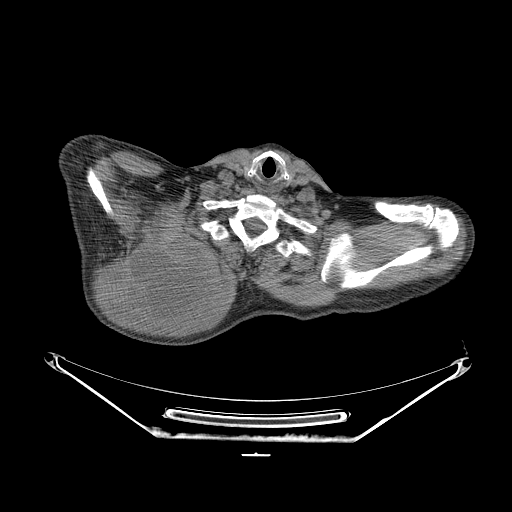
CT of an extremity soft-tissue mass (from a PET/CT study), one axial slice; slice 210 of 267 in the series (ordered by position); reconstruction kernel STANDARD; 140 kVp; soft-tissue window (W 400 / L 40 HU); 3.75 mm slice thickness; 512 × 512 image matrix, field of view 500 × 500 mm. Male patient. From the clinical record (not read from this slice): histological type: pleiomorphic spindle cell undifferentiated; grade: high; site of the primary tumour: right parascapusular.
Structures marked on this image (expert contour drawn on MRI and transferred to this co-registered scan by the dataset authors):
- gross tumour volume including surrounding oedema: bounding box (x1, y1, x2, y2) in pixels: (96, 235, 236, 325)
- gross tumour volume (mass): (100, 237, 220, 321)